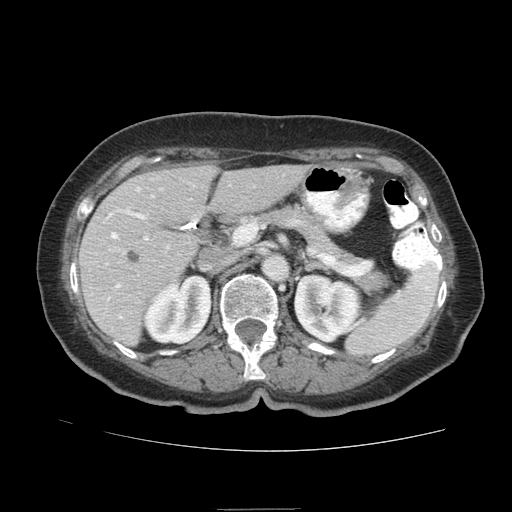
Contrast-enhanced abdominal CT (liver protocol), one axial slice; slice 41 of 95 in the series (ordered by position); soft-tissue window (W 400 / L 40 HU); 2.5 mm slice thickness; 512 × 512 image matrix. From the clinical record (not read from this slice): diagnosis: hepatocellular carcinoma (patient treated with transarterial chemoembolisation; whether this scan precedes or follows treatment is not stated here); TNM stage (as recorded): Stage-IVA.
Structures marked on this image (semi-automatic segmentation, software-assisted and operator-edited):
- liver parenchyma outside the tumour (the mass and vessels are separate outlines, so this box may not span the whole liver): bounding box [x1, y1, x2, y2] px = [78, 164, 309, 344]
- liver vessels: [108, 188, 198, 319]